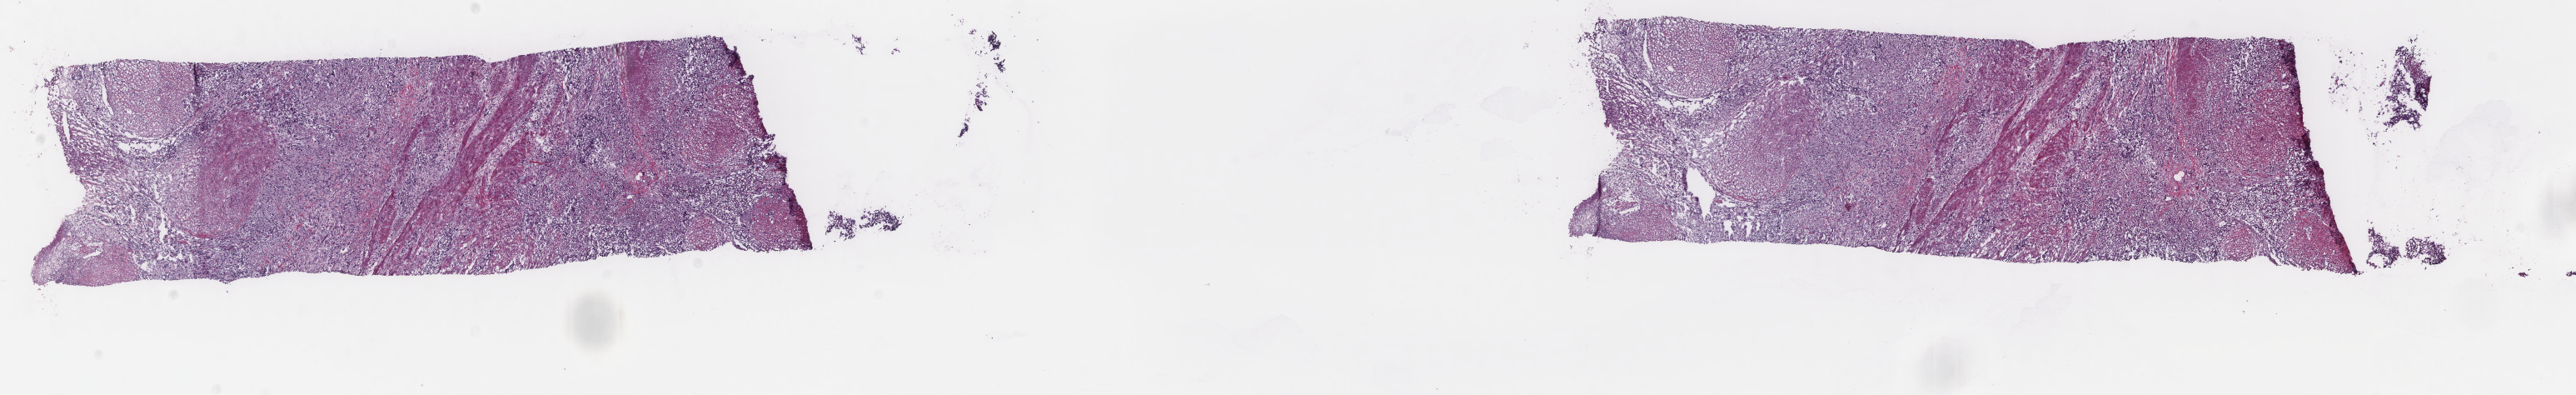
Digitized H&E tissue section (whole slide) — shown as a low-resolution overview of the whole scanned area (about 24.6 x 3.8 mm, acquisition: 40x scan). Frozen section from the top of the tissue portion. Primary tumour sample from the bladder. Male, age 60 years at initial diagnosis. Histologic grade: high grade. Composition of this section per pathologist review: tumour cells 80%, tumour nuclei 70%, normal cells 20%, stromal cells 0%, necrosis 0%. Inflammatory infiltration, as recorded: lymphocyte infiltration 0%, monocyte infiltration 0%, neutrophil infiltration 0%.
• histologic diagnosis: Transitional cell carcinoma
• TNM: T3b N0 MX
• lymph nodes positive (case pathology): 0 of 48 examined
• AJCC pathologic stage: III (7th edition)